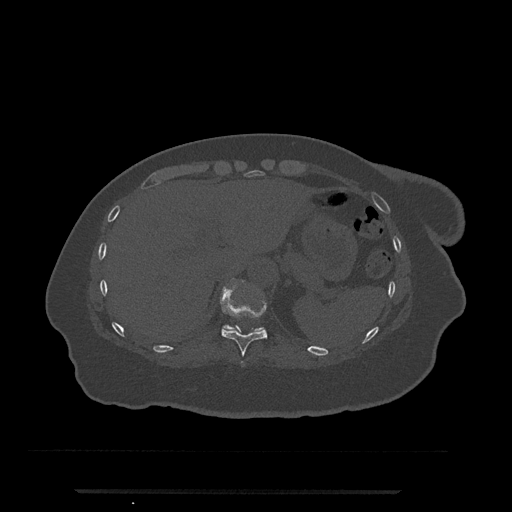
CT including the spine, one axial slice. Reconstruction kernel Br40s/3. Bone window (W 1800 / L 400 HU). 0.5 mm slice thickness. 512 × 512 image matrix, field of view 440 × 440 mm. Patient: female, 51 years. Case-level facts recorded for this patient, not image findings: primary cancer: neuro; vertebrae with lytic lesions (as recorded): T8.
Structures marked on this image (semi-automatically segmented with operator editing):
- T10 vertebra: bounding box [x1, y1, x2, y2] px = [220, 278, 267, 364]
- T11 vertebra: [224, 325, 262, 331]